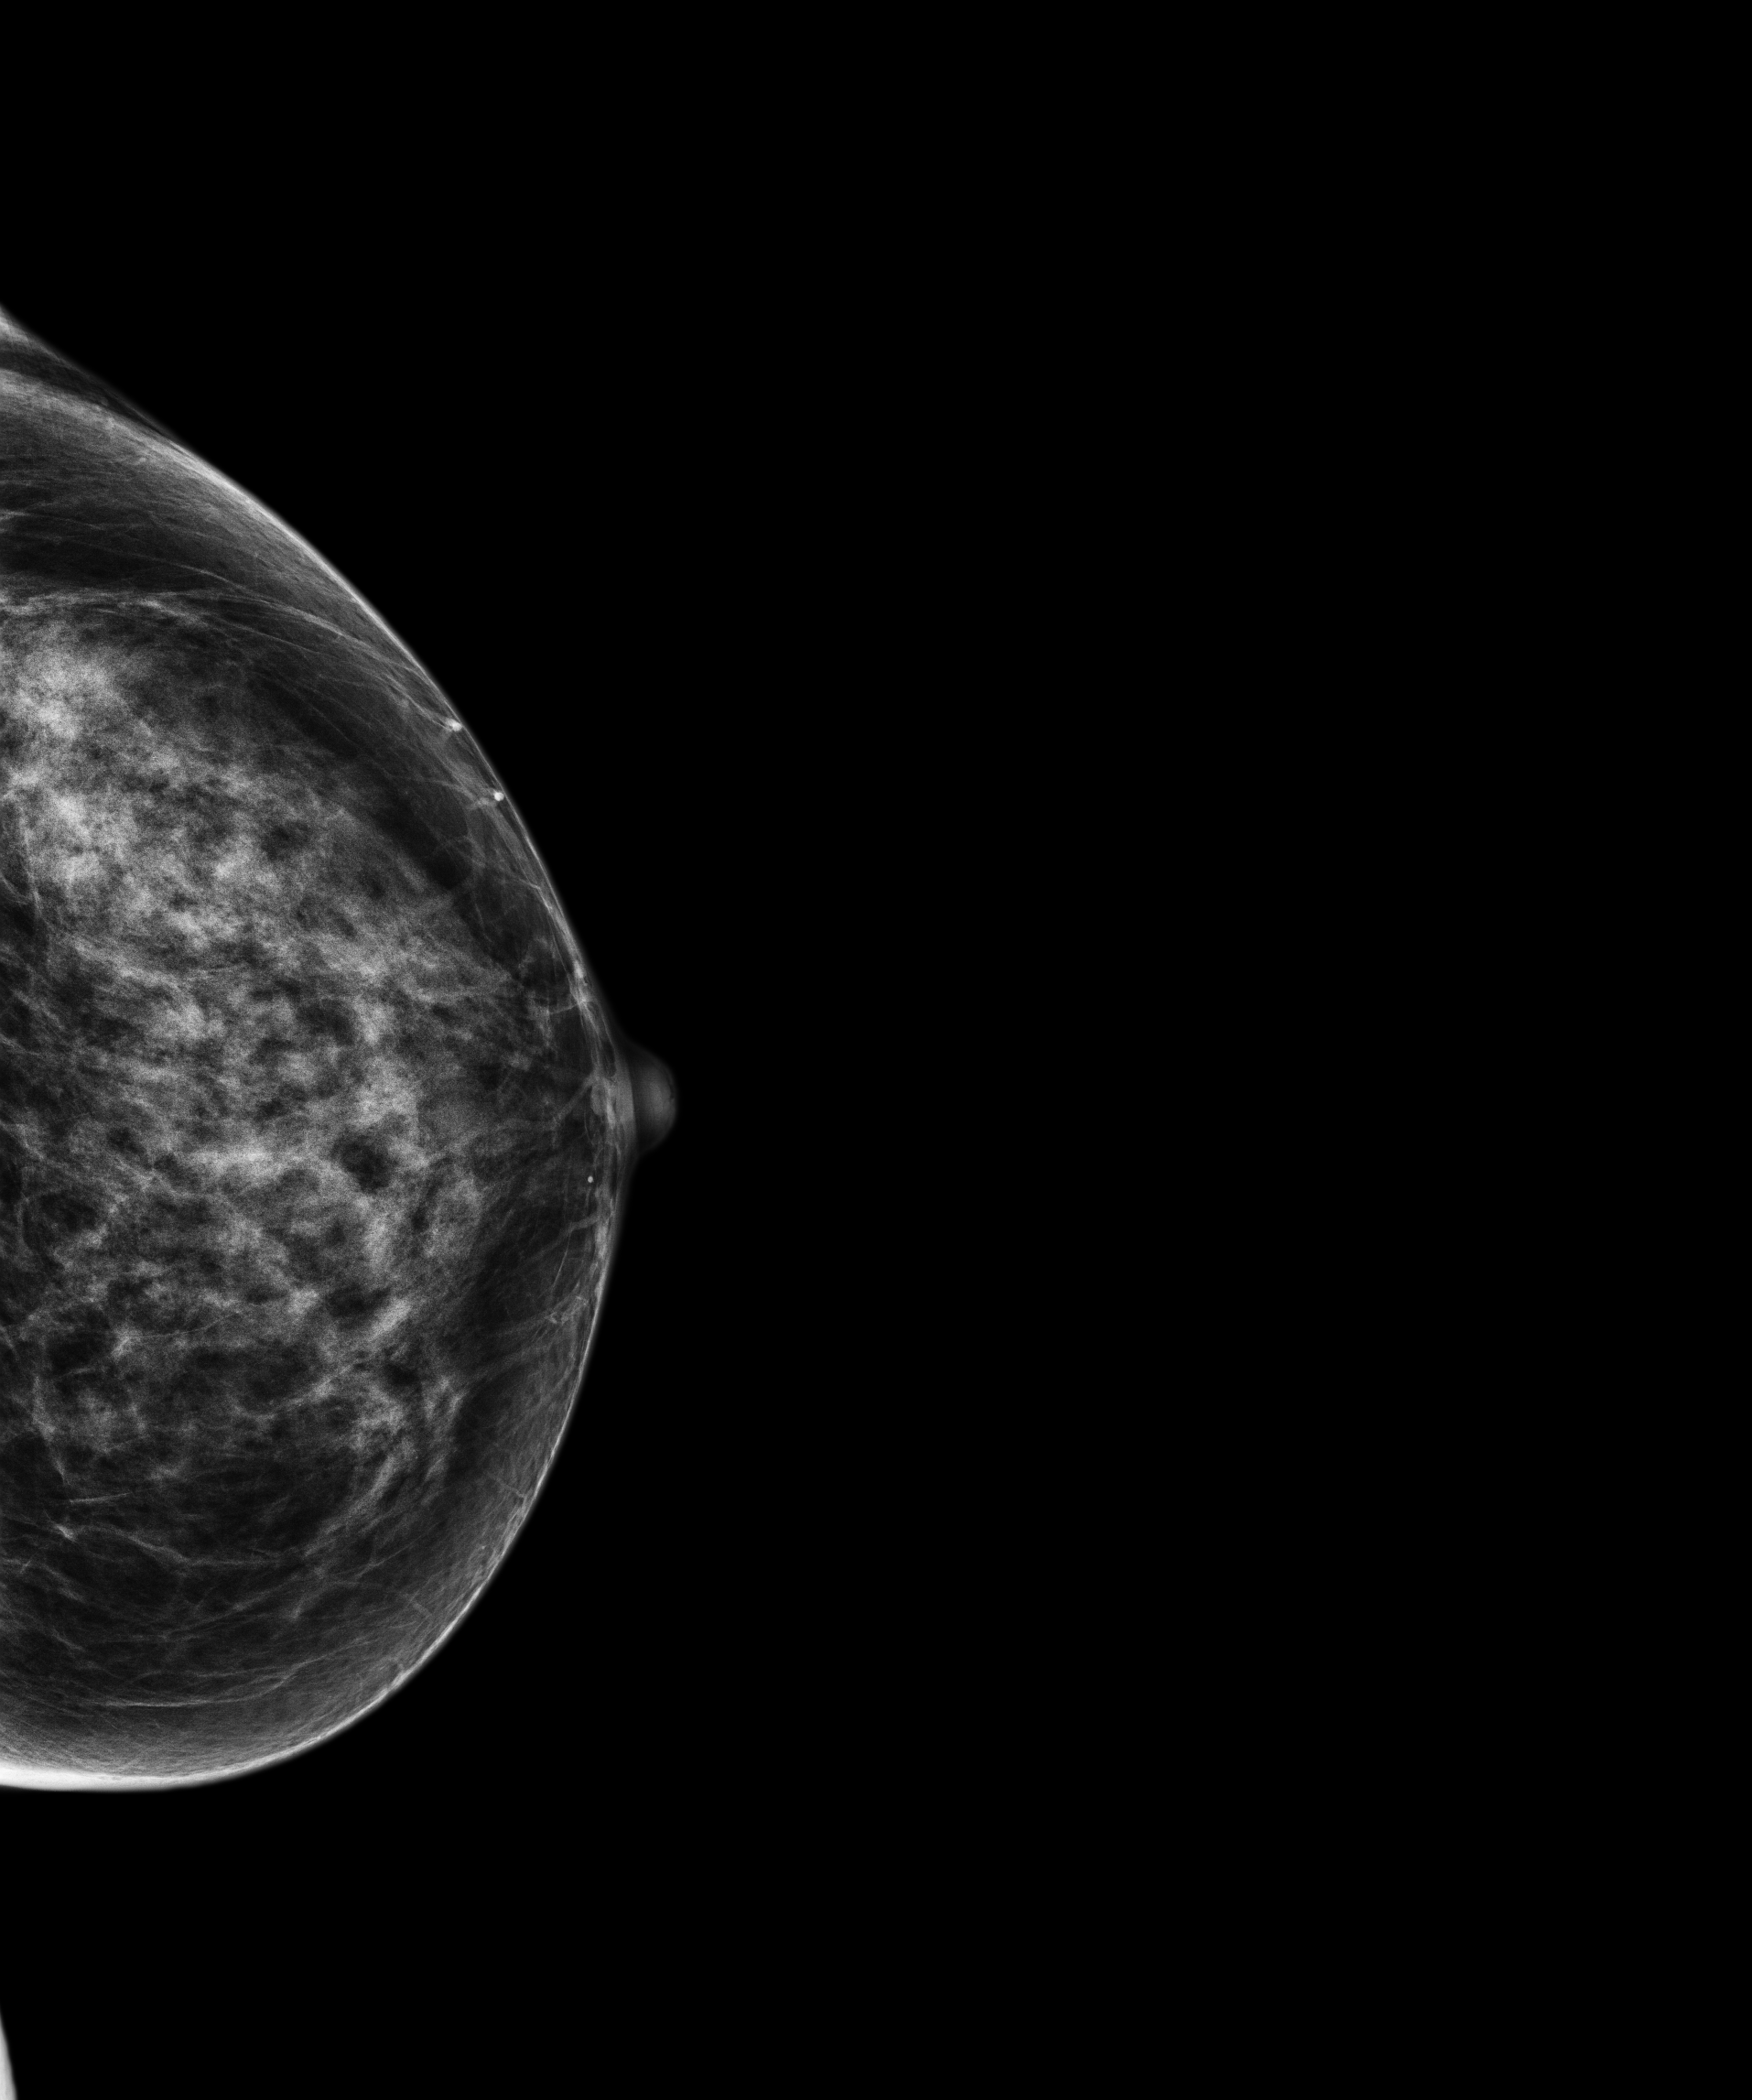
Screening examination; compressed breast thickness 53.1 mm. Patient: female, 57 years.
Image type: full-field digital mammogram. Breast: left. Projection: cranio-caudal projection.